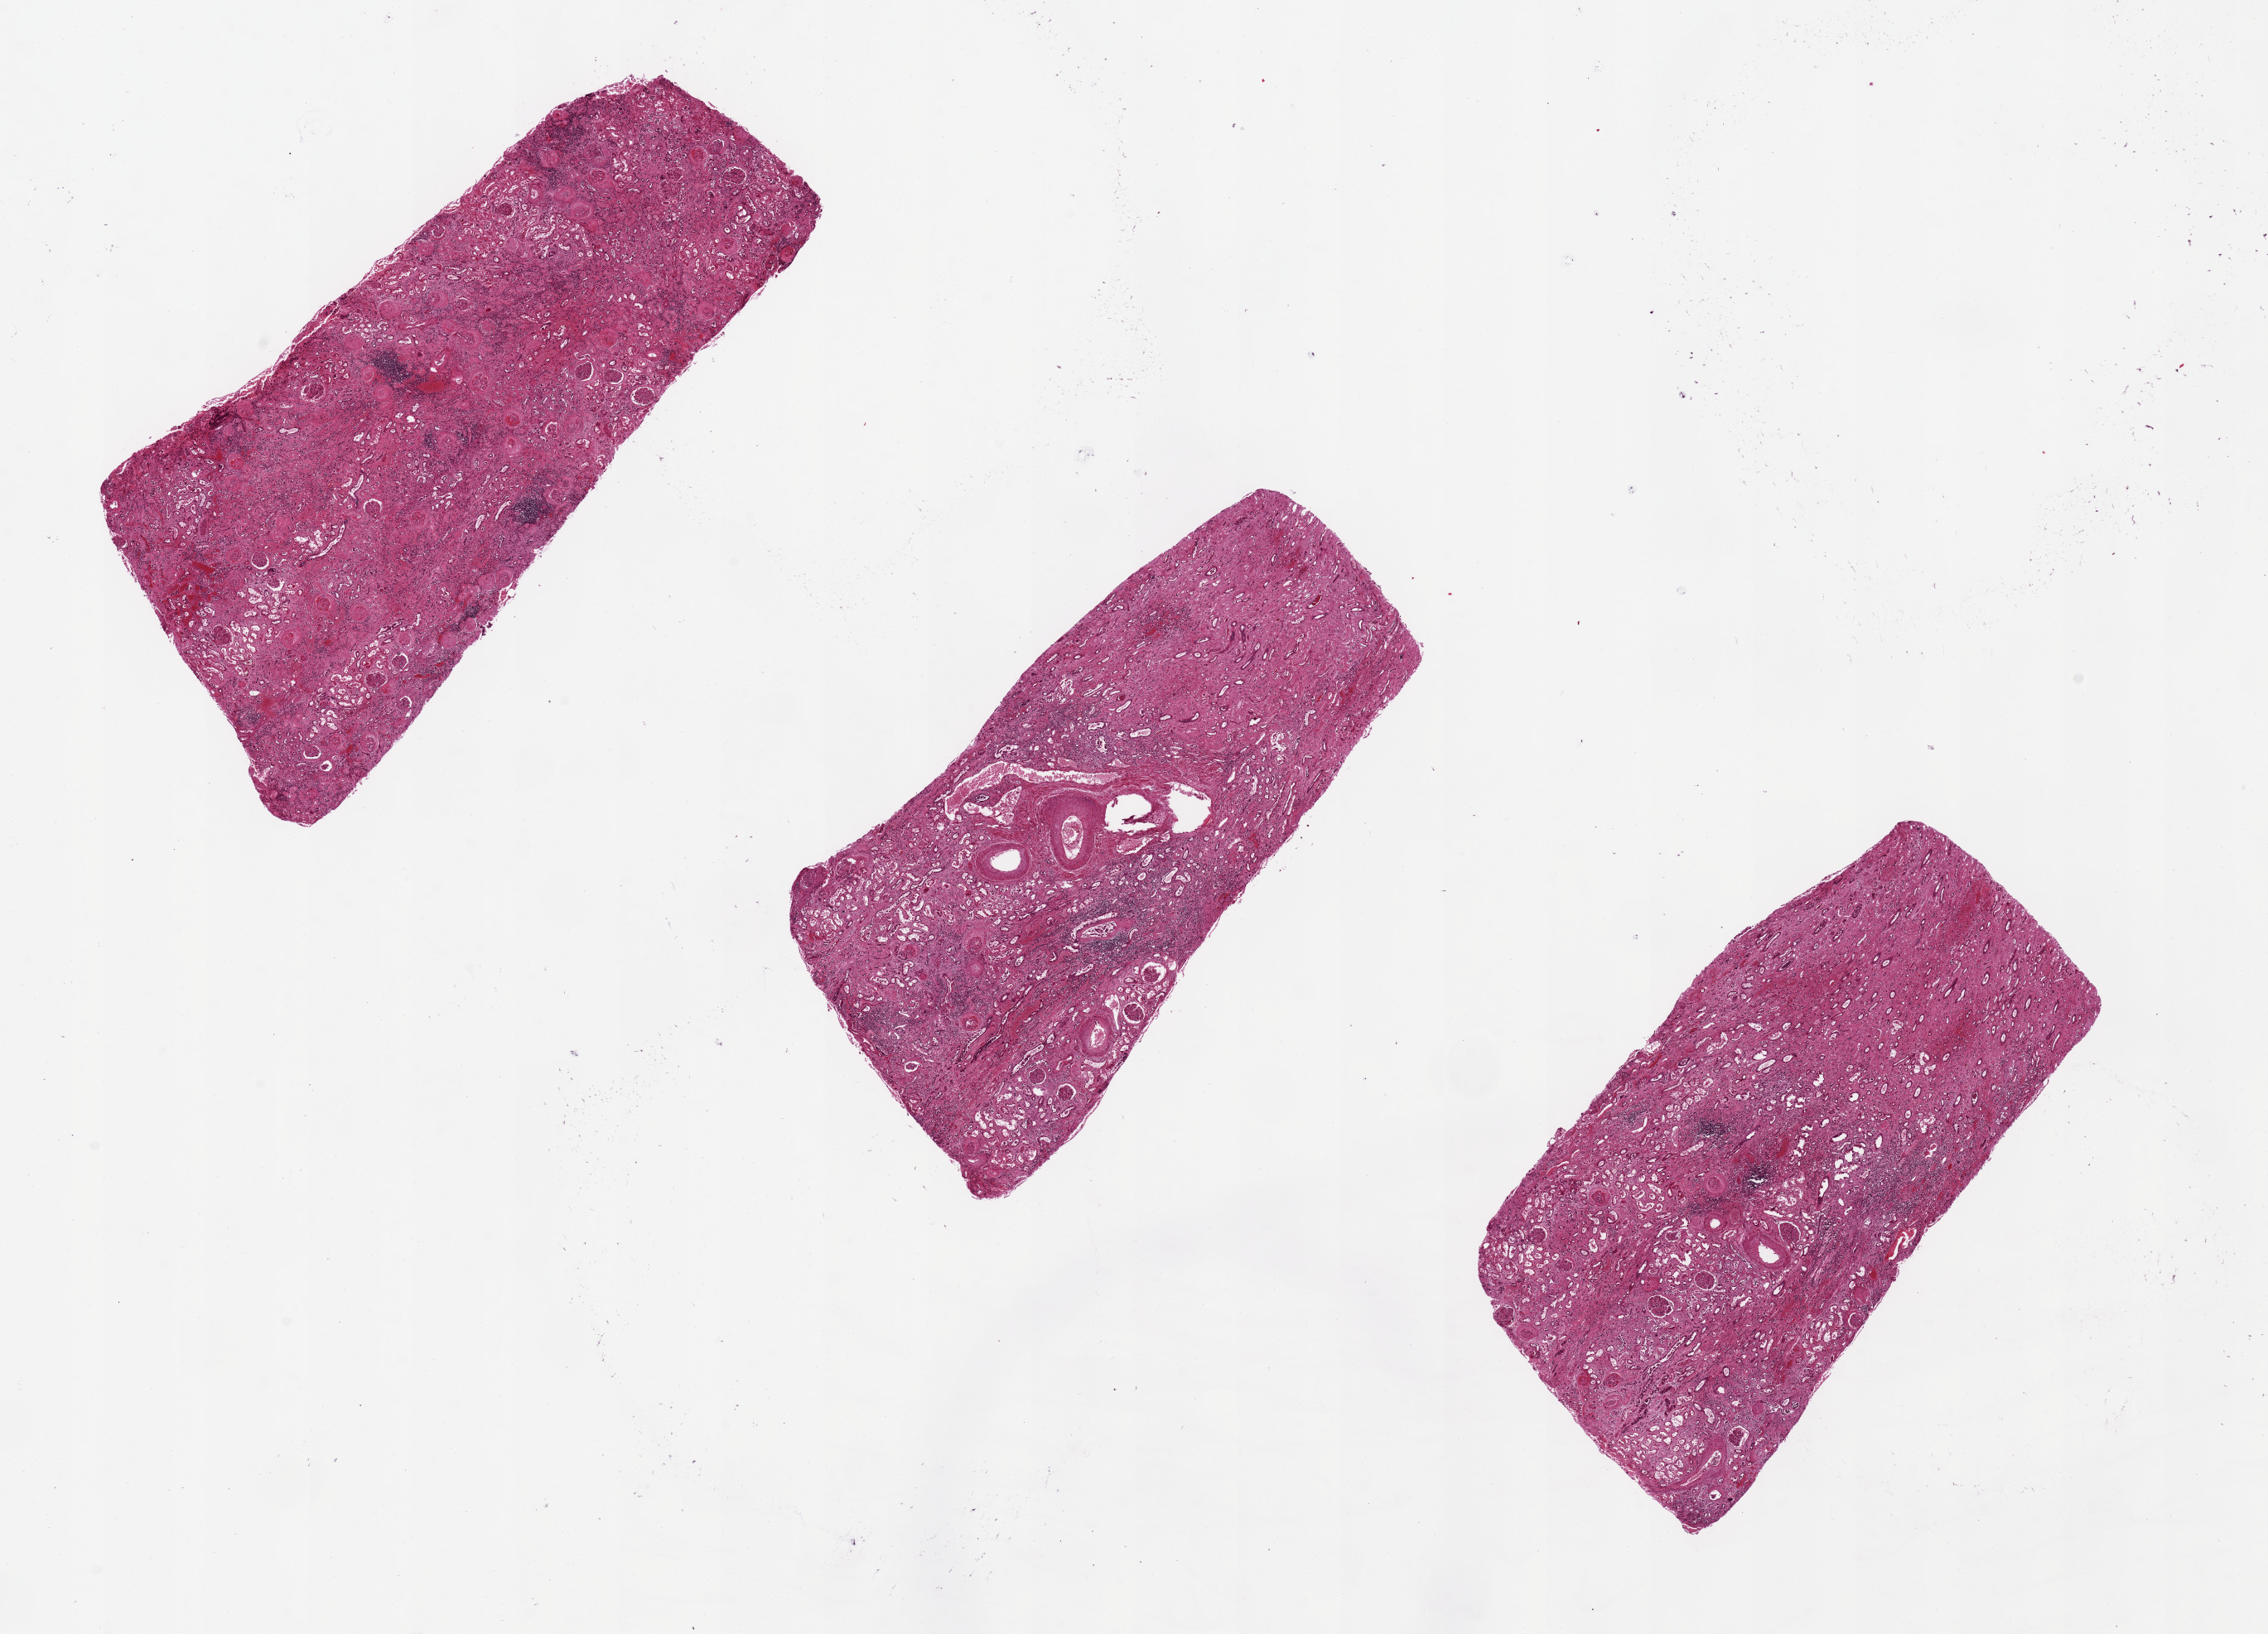
Digitized haematoxylin and eosin-stained section — whole scanned area (about 21.7 x 15.6 mm) shown as a low-resolution overview, PAXgene-fixed paraffin-embedded (PFPE) section, target tissue: renal cortex, tissue donor sample. Donor sex: male.
Reviewer comment on this tissue sample: Severe arterial, arteriolar, and glomerular sclerosis, chronic inflammation and fibrosis.